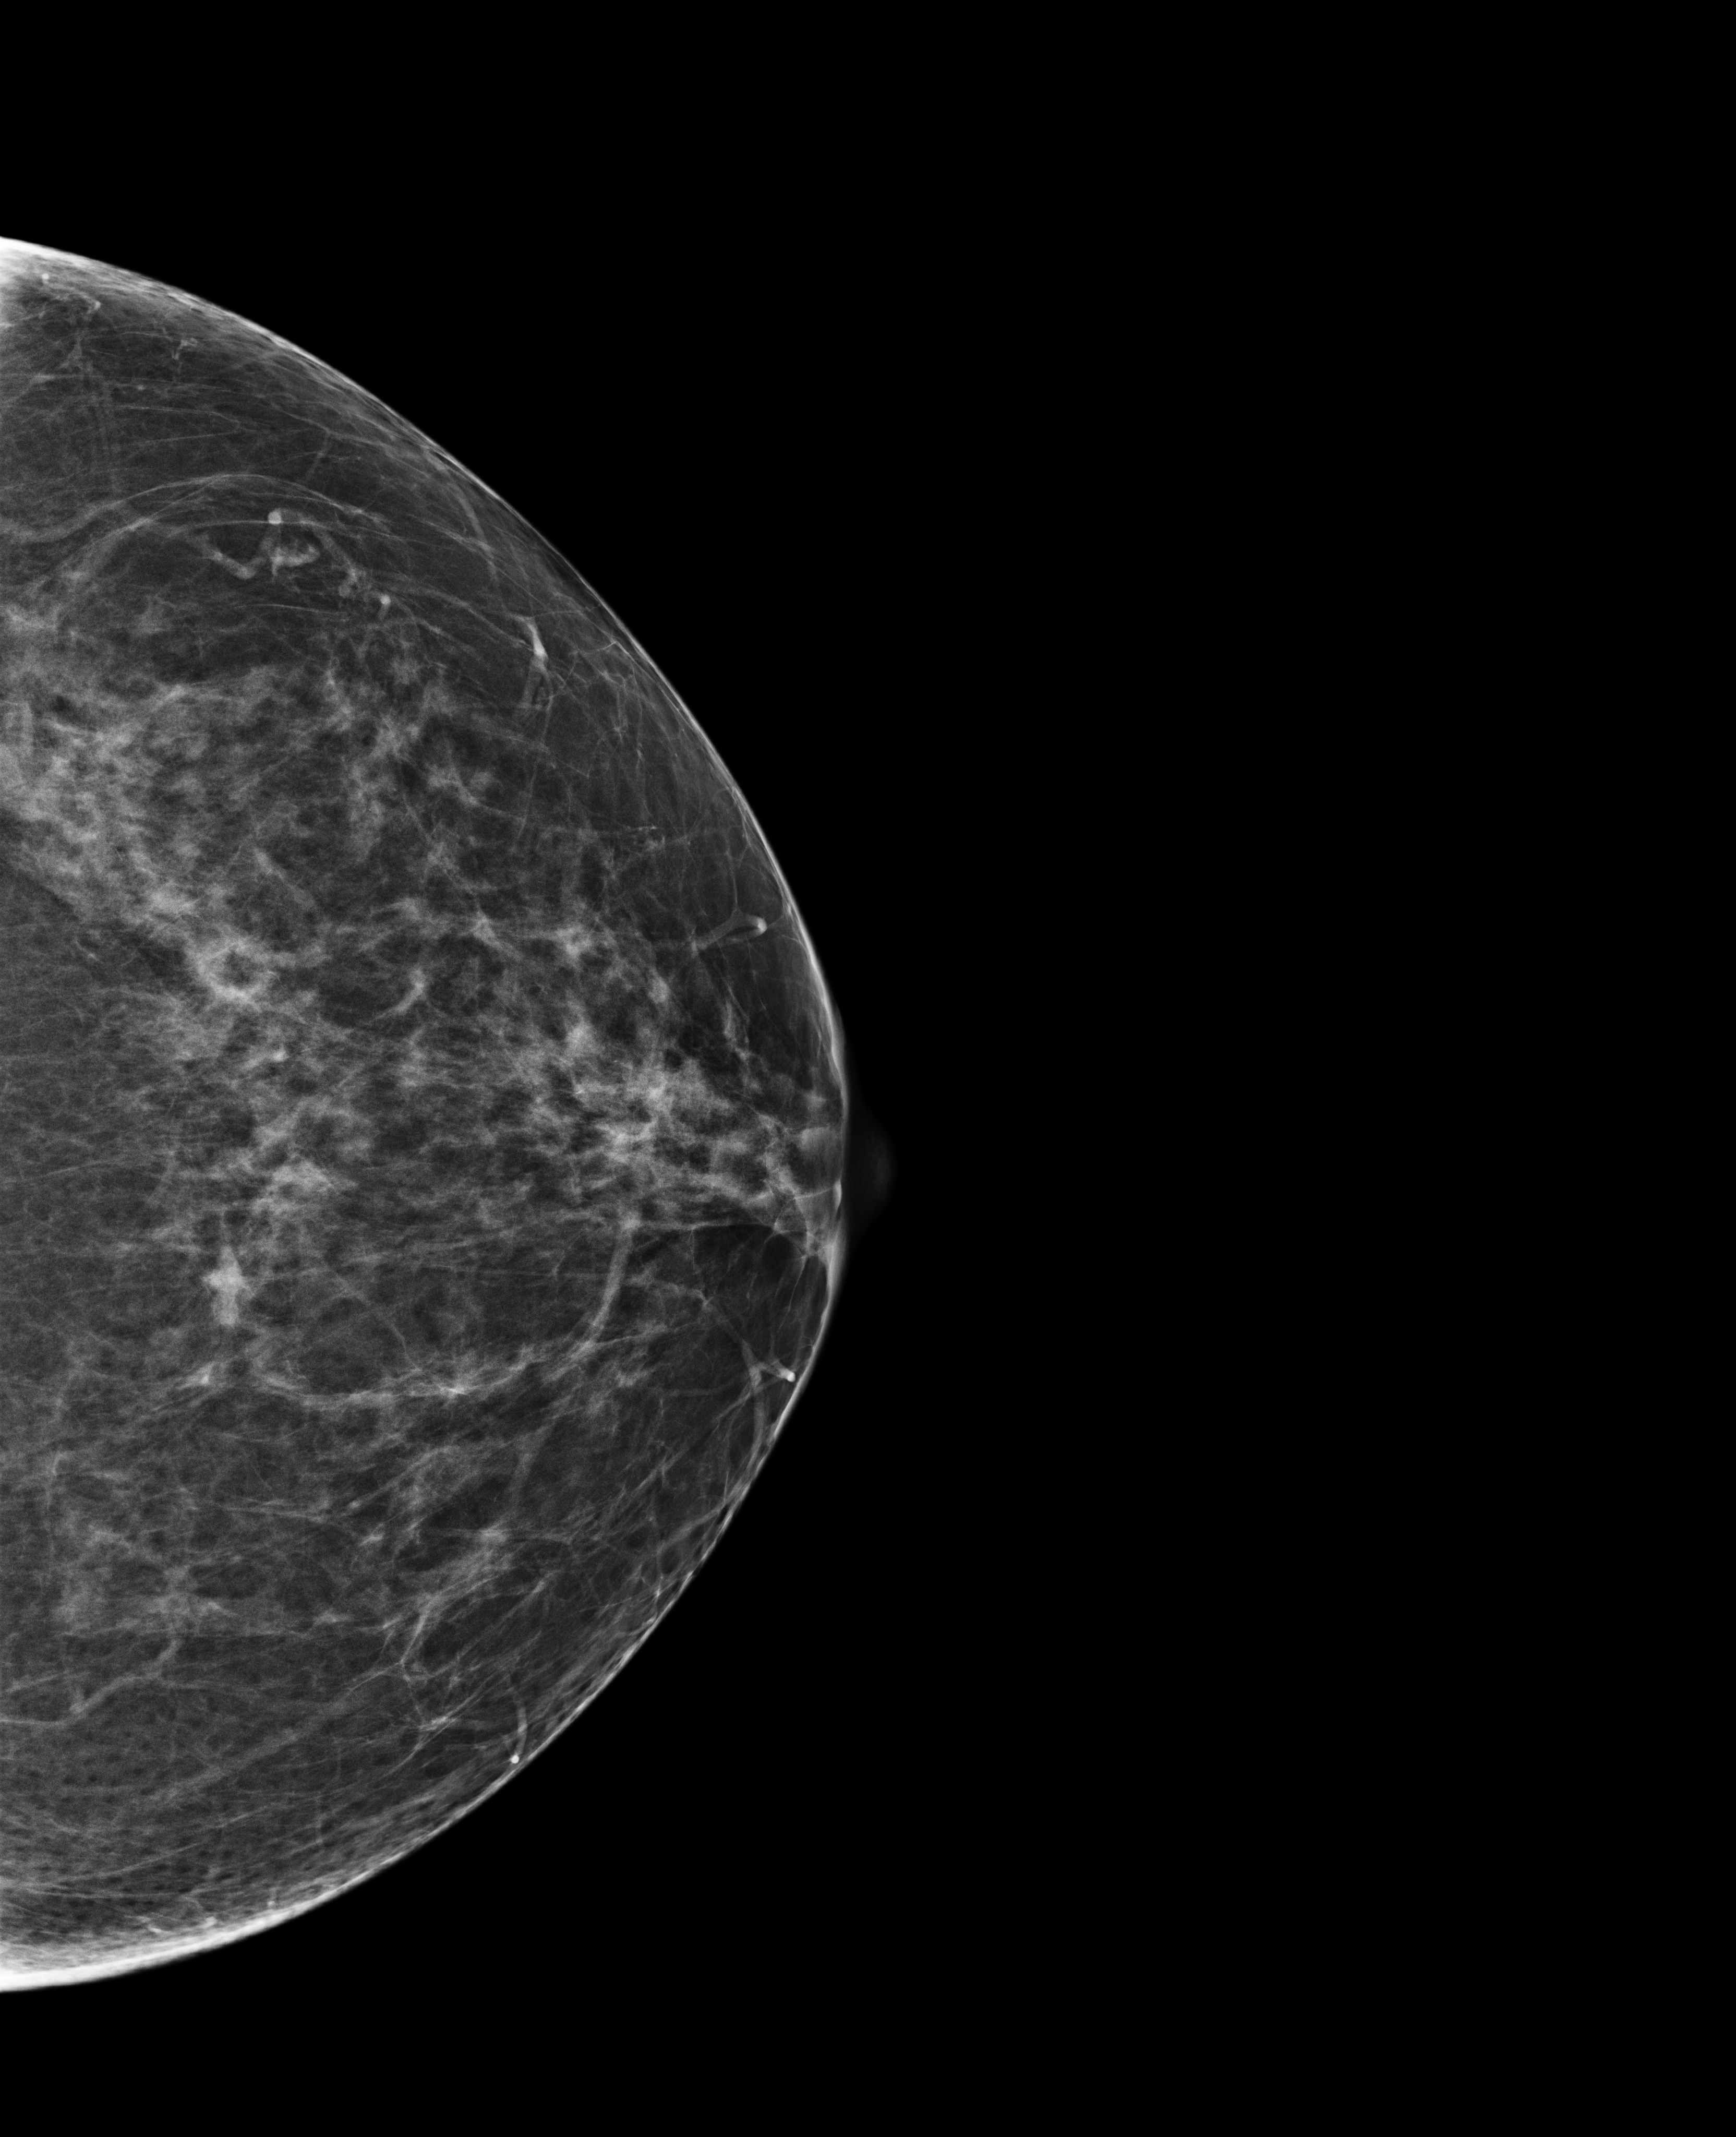
Screening examination; compressed breast thickness 73 mm. Female patient, age 60 years.
Image type: full-field digital mammogram. Breast: left. Projection: cranio-caudal projection.